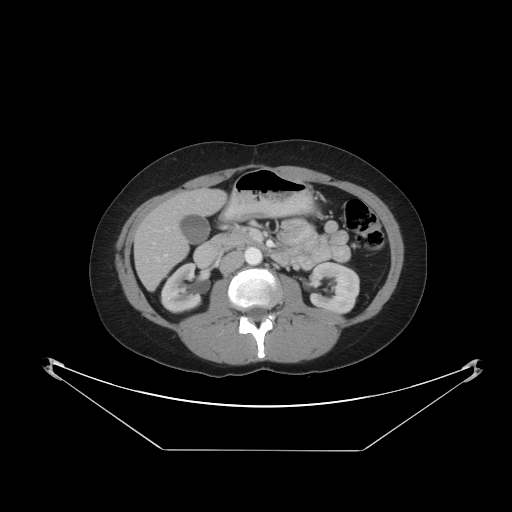
Contrast-enhanced abdominal CT, one axial slice; position 17 of 48 along the scan axis; reconstruction kernel STANDARD; 120 kVp; intravenous contrast given; soft-tissue window (W 400 / L 40 HU); 5 mm slice thickness; 512 × 512 image matrix, field of view 482 × 482 mm. Female patient, age 38 years. From the clinical record (not read from this slice): diagnosis: colorectal cancer liver metastases, imaged before liver resection; multiple liver metastases: yes; largest metastasis: 2.5 cm; disease in both lobes: no.
Outlined on this slice (manually delineated by an expert):
- hepatic veins: bounding box (x1, y1, x2, y2) in pixels: (165, 226, 169, 231)
- liver: (135, 189, 225, 289)
- planned liver remnant (the part of the liver to remain after resection): (171, 189, 225, 215)
- portal vein (with intrahepatic branches): (156, 254, 167, 261)